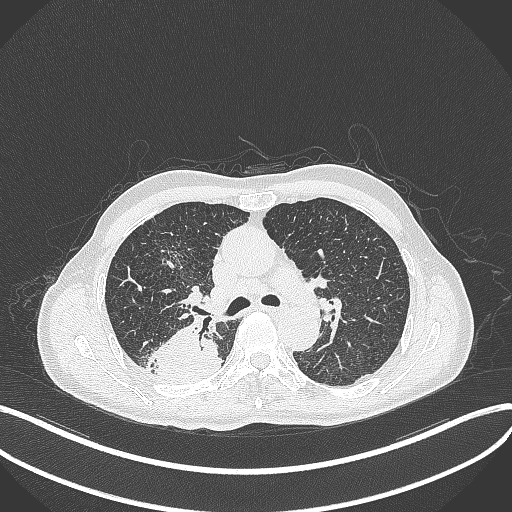
Chest CT, one axial slice. Slice 294 of 428 in the series (ordered by position). Lung window (W 1500 / L -600 HU). 512 × 512 image matrix, field of view 400 × 400 mm. Male patient, age 79 years. From the clinical record (not read from this slice): clinical TNM (as recorded): T3 N0 M0.
Annotated regions visible in this slice (bounding box drawn by a radiologist):
- lung tumour (recorded histology: adenocarcinoma): bounding box (x1, y1, x2, y2) in pixels: (144, 321, 223, 383)